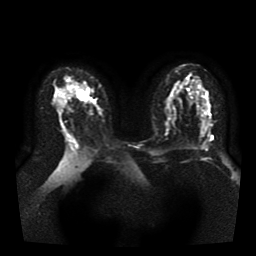
Breast MRI, one axial slice; slice 24 of 41 in the series (ordered by position); diffusion-weighted series; image 2 of 4 stored at this slice position (different b-values; order by instance number); 1.5 T; 5 mm slice thickness; 256 × 256 image matrix, field of view 330 × 330 mm. Female patient.
Structures marked on this image (outlined manually by an expert reader):
- tumour on diffusion-weighted imaging: bounding box [x1, y1, x2, y2] px = [77, 90, 90, 101]